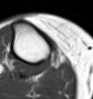
MRI of an extremity soft-tissue mass, one axial slice. Slice 39 of 54 in the series (ordered by position). MR volume resampled by the dataset authors to the PET/CT grid (not the native acquisition matrix). 93 × 99 image matrix. Female patient. Case-level facts recorded for this patient, not image findings: histological type: undifferentiated – high grade; grade: high; site of the primary tumour: right thigh.
Outlined on this slice (expert contour drawn on MRI and transferred to this co-registered scan by the dataset authors):
- gross tumour volume (mass): bounding box [x1, y1, x2, y2] px = [50, 54, 60, 67]